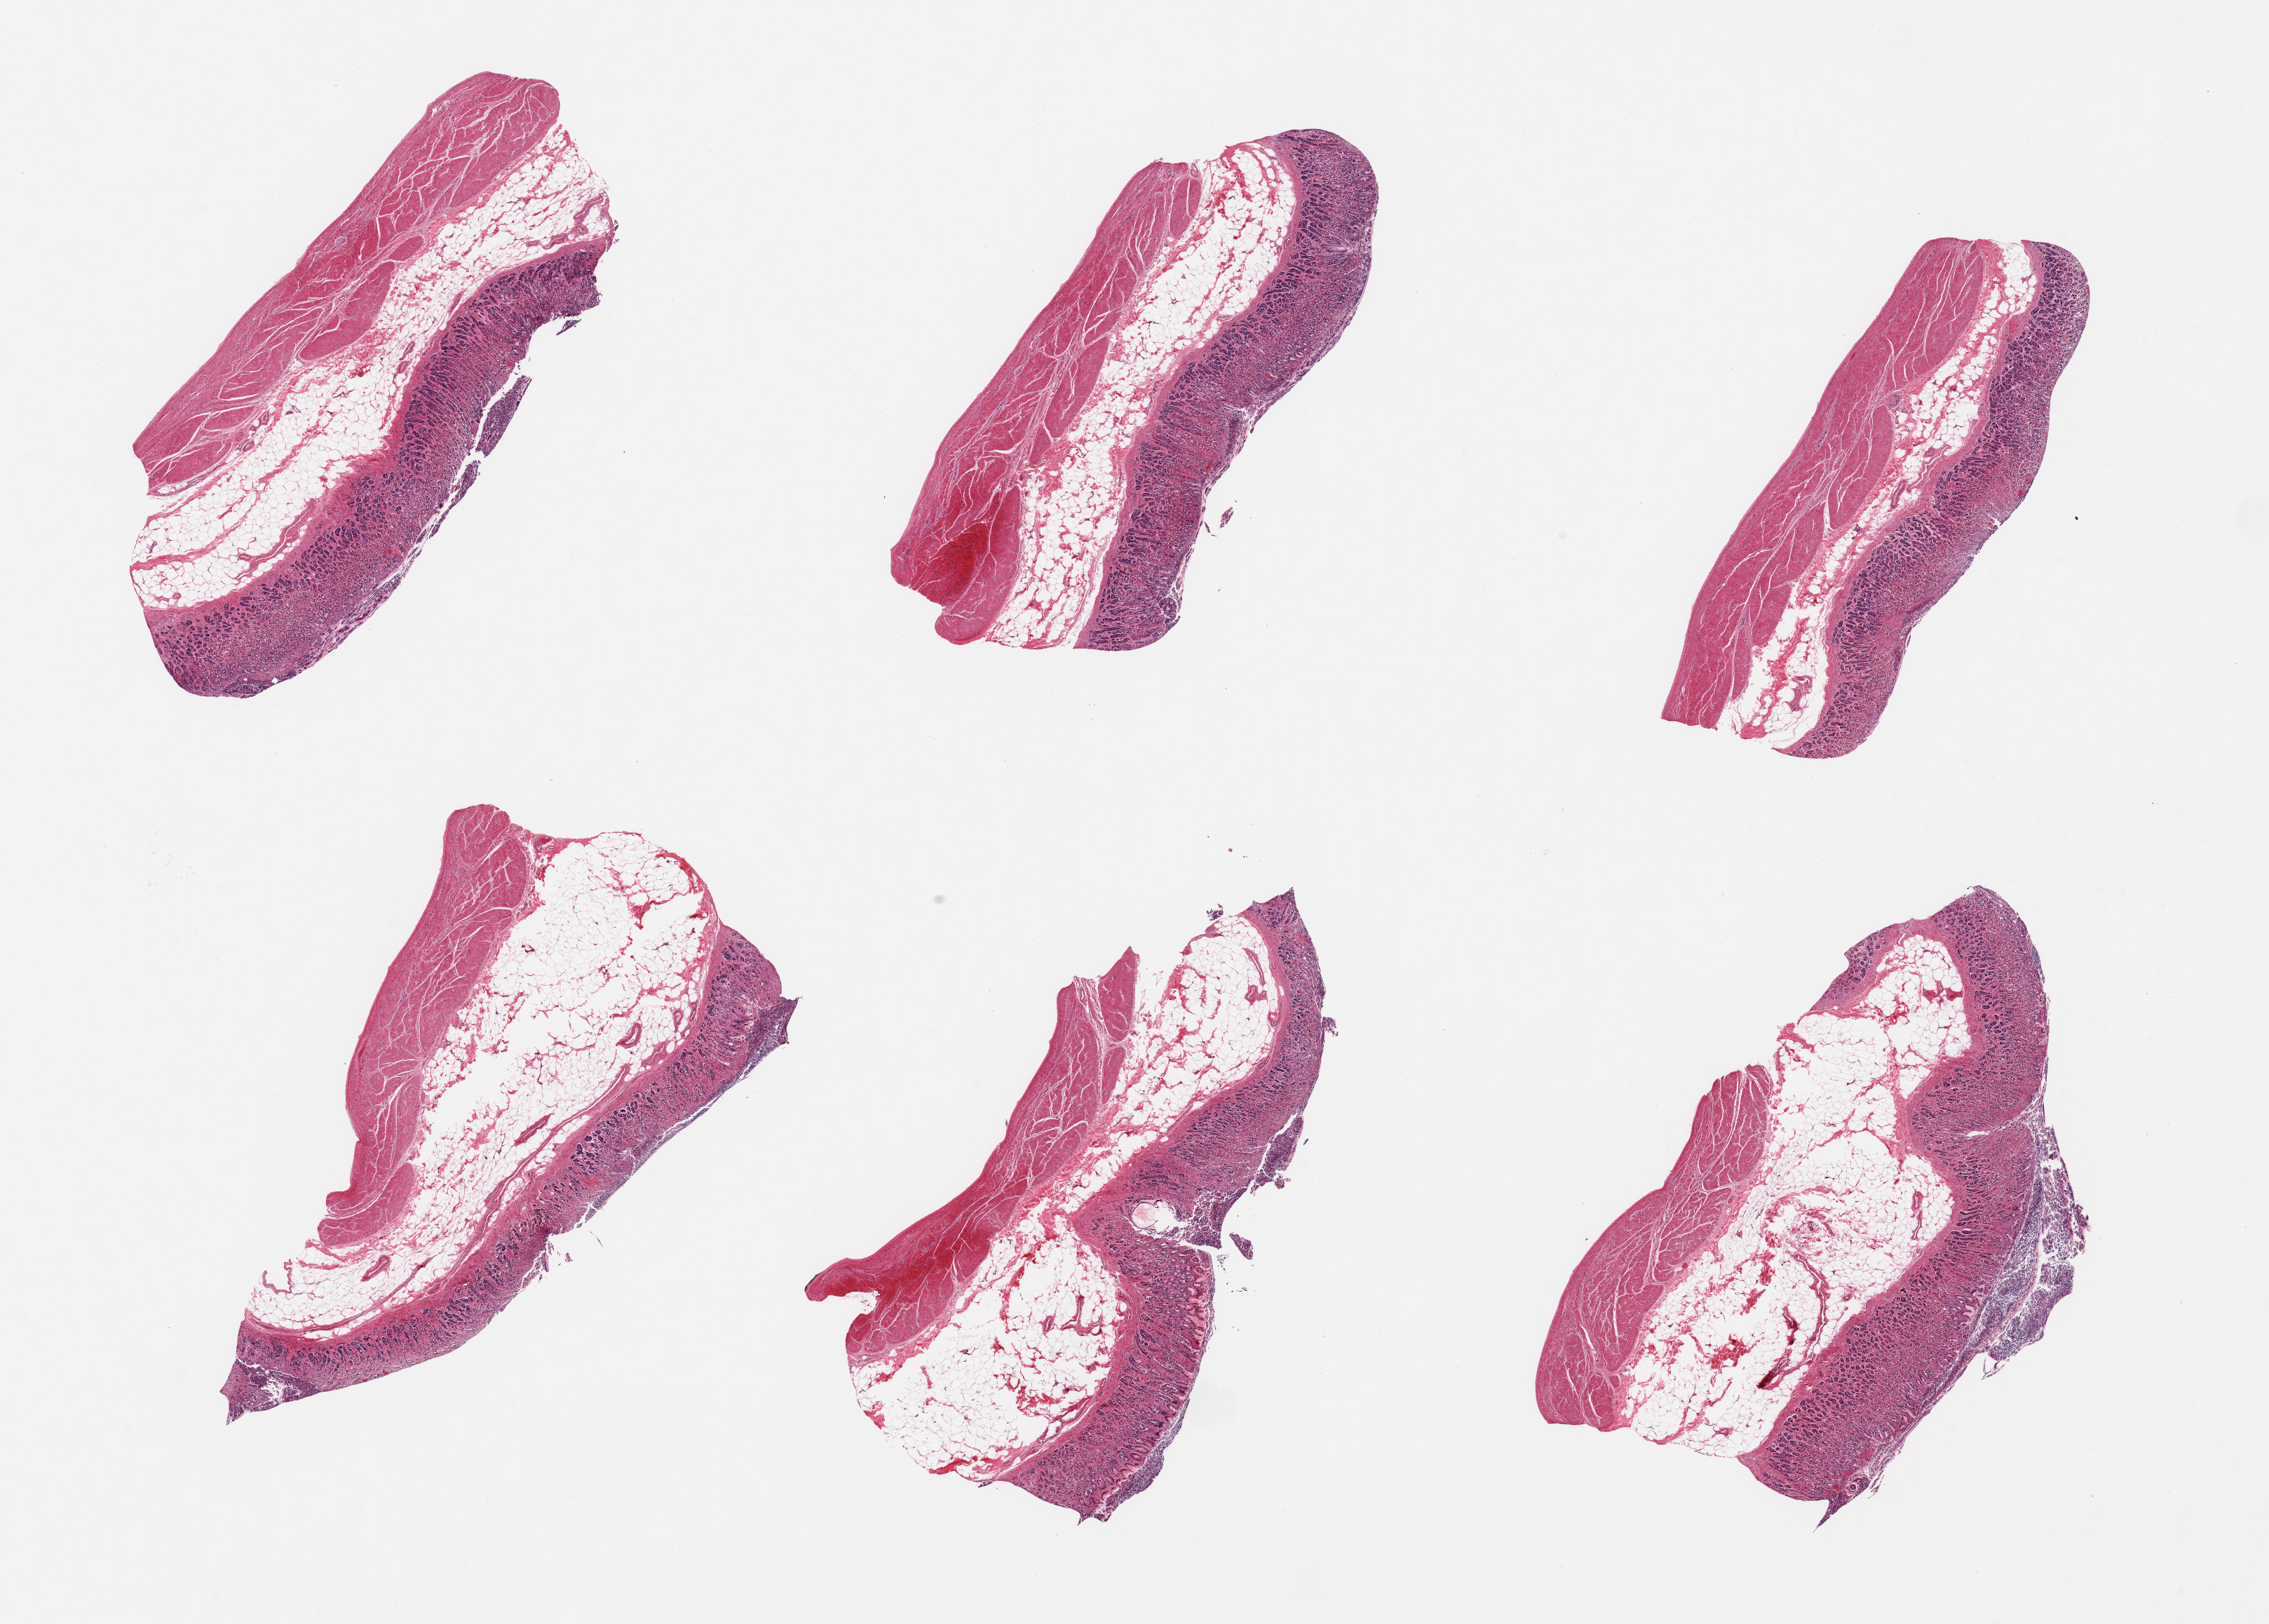
Hematoxylin and eosin (H&E) whole-slide image — low-resolution overview of the scanned area, about 25.6 x 18.3 mm, PAXgene-fixed paraffin-embedded (PFPE) section, sampled site (target tissue): stomach, tissue donor sample. Male donor.
* reviewer comment on this tissue sample: 6 pieces, mucosa with moderately advanced autolysis, up to ~1mm, ~30-40% thickness